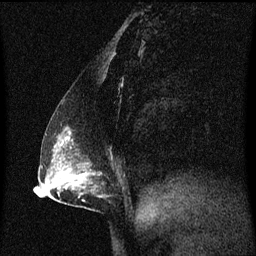
Breast MRI (dynamic contrast-enhanced), one sagittal slice. Slice 35 of 60 in the series (ordered by position). Dynamic contrast-enhanced series, image 2 of 3 at this slice position (ordered by acquisition). 1.5 T. TE 4.2 ms, TR 8.4 ms. 2 mm slice thickness. 256 × 256 image matrix, field of view 200 × 200 mm. Patient: female, 40 years. Case-level facts recorded for this patient, not image findings: setting: breast cancer imaged before/during neoadjuvant chemotherapy; receptor status: triple-negative.
Annotated regions visible in this slice (semi-automatically segmented with operator editing):
- analysis volume of interest (the breast-tissue region the enhancement analysis was run in; not a lesion): box from (x=58, y=126) to (x=105, y=211) px
- tumour enhancement mask (voxels above the 70 % enhancement threshold inside the analysis volume of interest): (x=64, y=136)–(x=69, y=141)